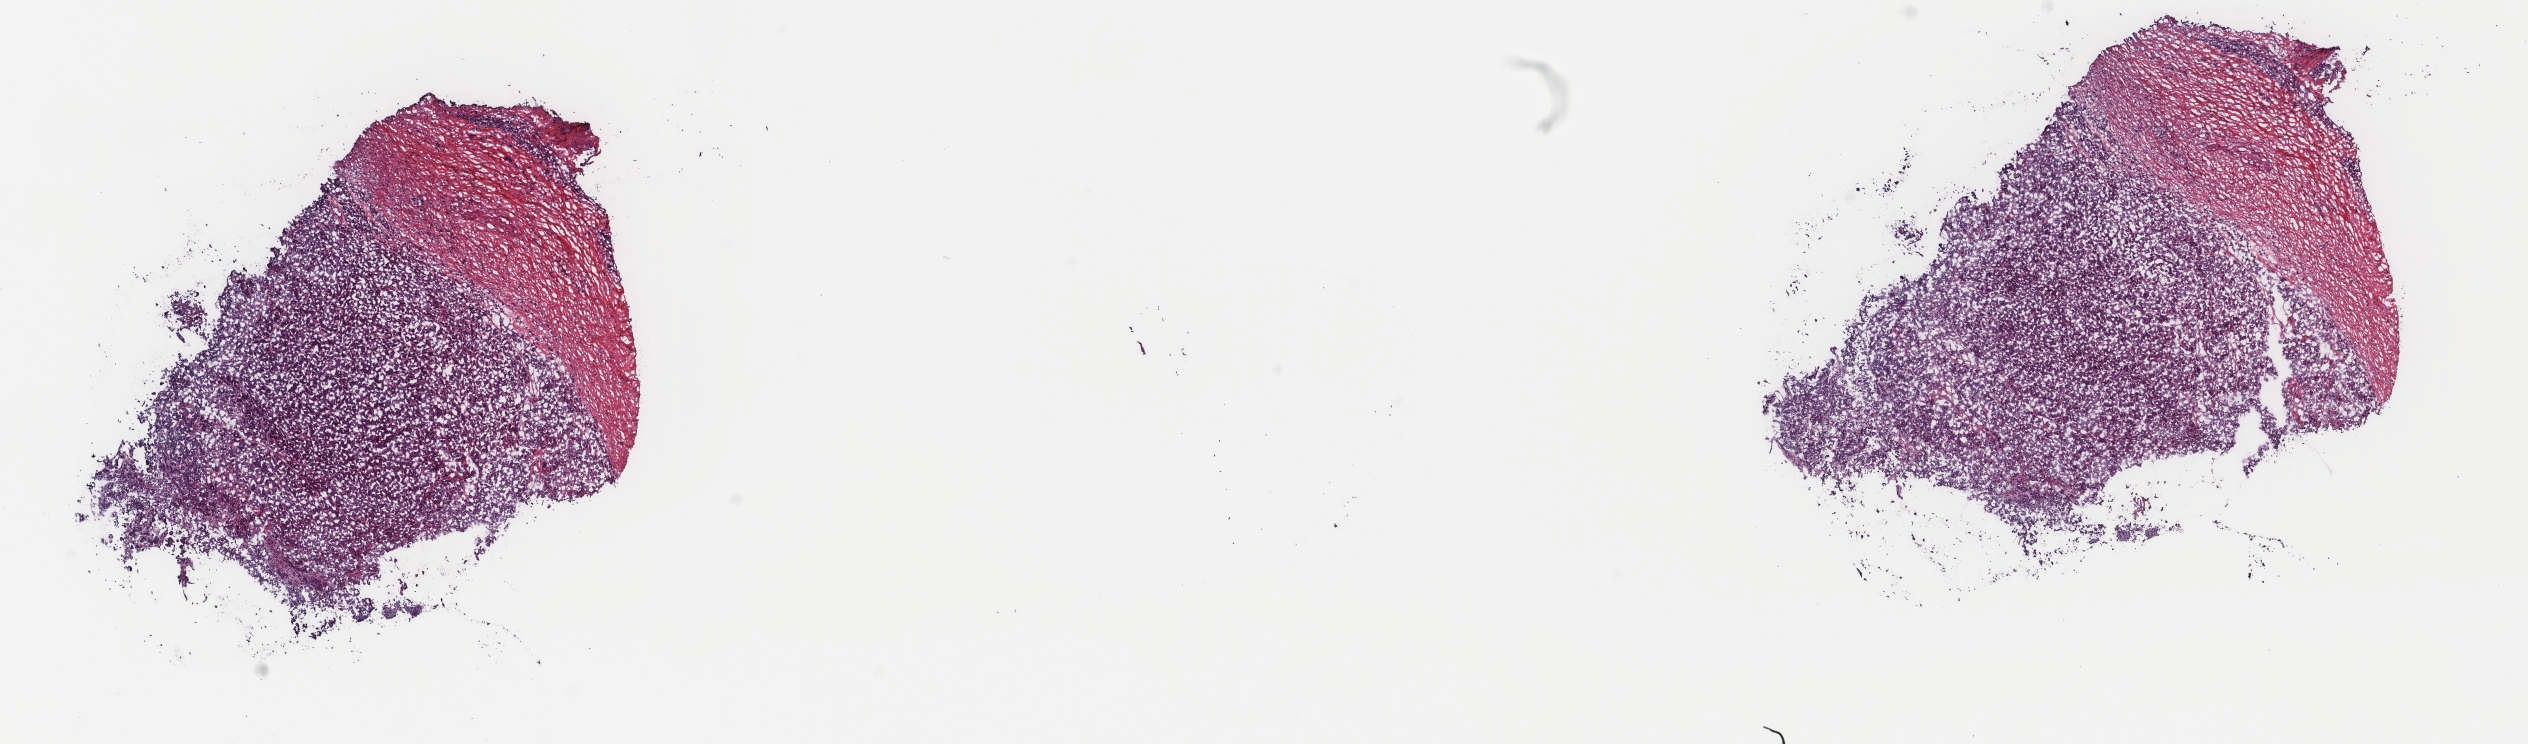
H&E whole-slide image, a low-resolution overview of the entire scanned area, about 20.1 x 5.9 mm (from a 40x scan). Frozen section from the top of the tissue portion. Primary tumour sample from the thyroid. Female patient; age at initial diagnosis 55 years. Pathologist review of this section (percent, as recorded): tumour cells 70%, tumour nuclei 100%.
Diagnosis: Papillary carcinoma, follicular variant (thyroid gland).